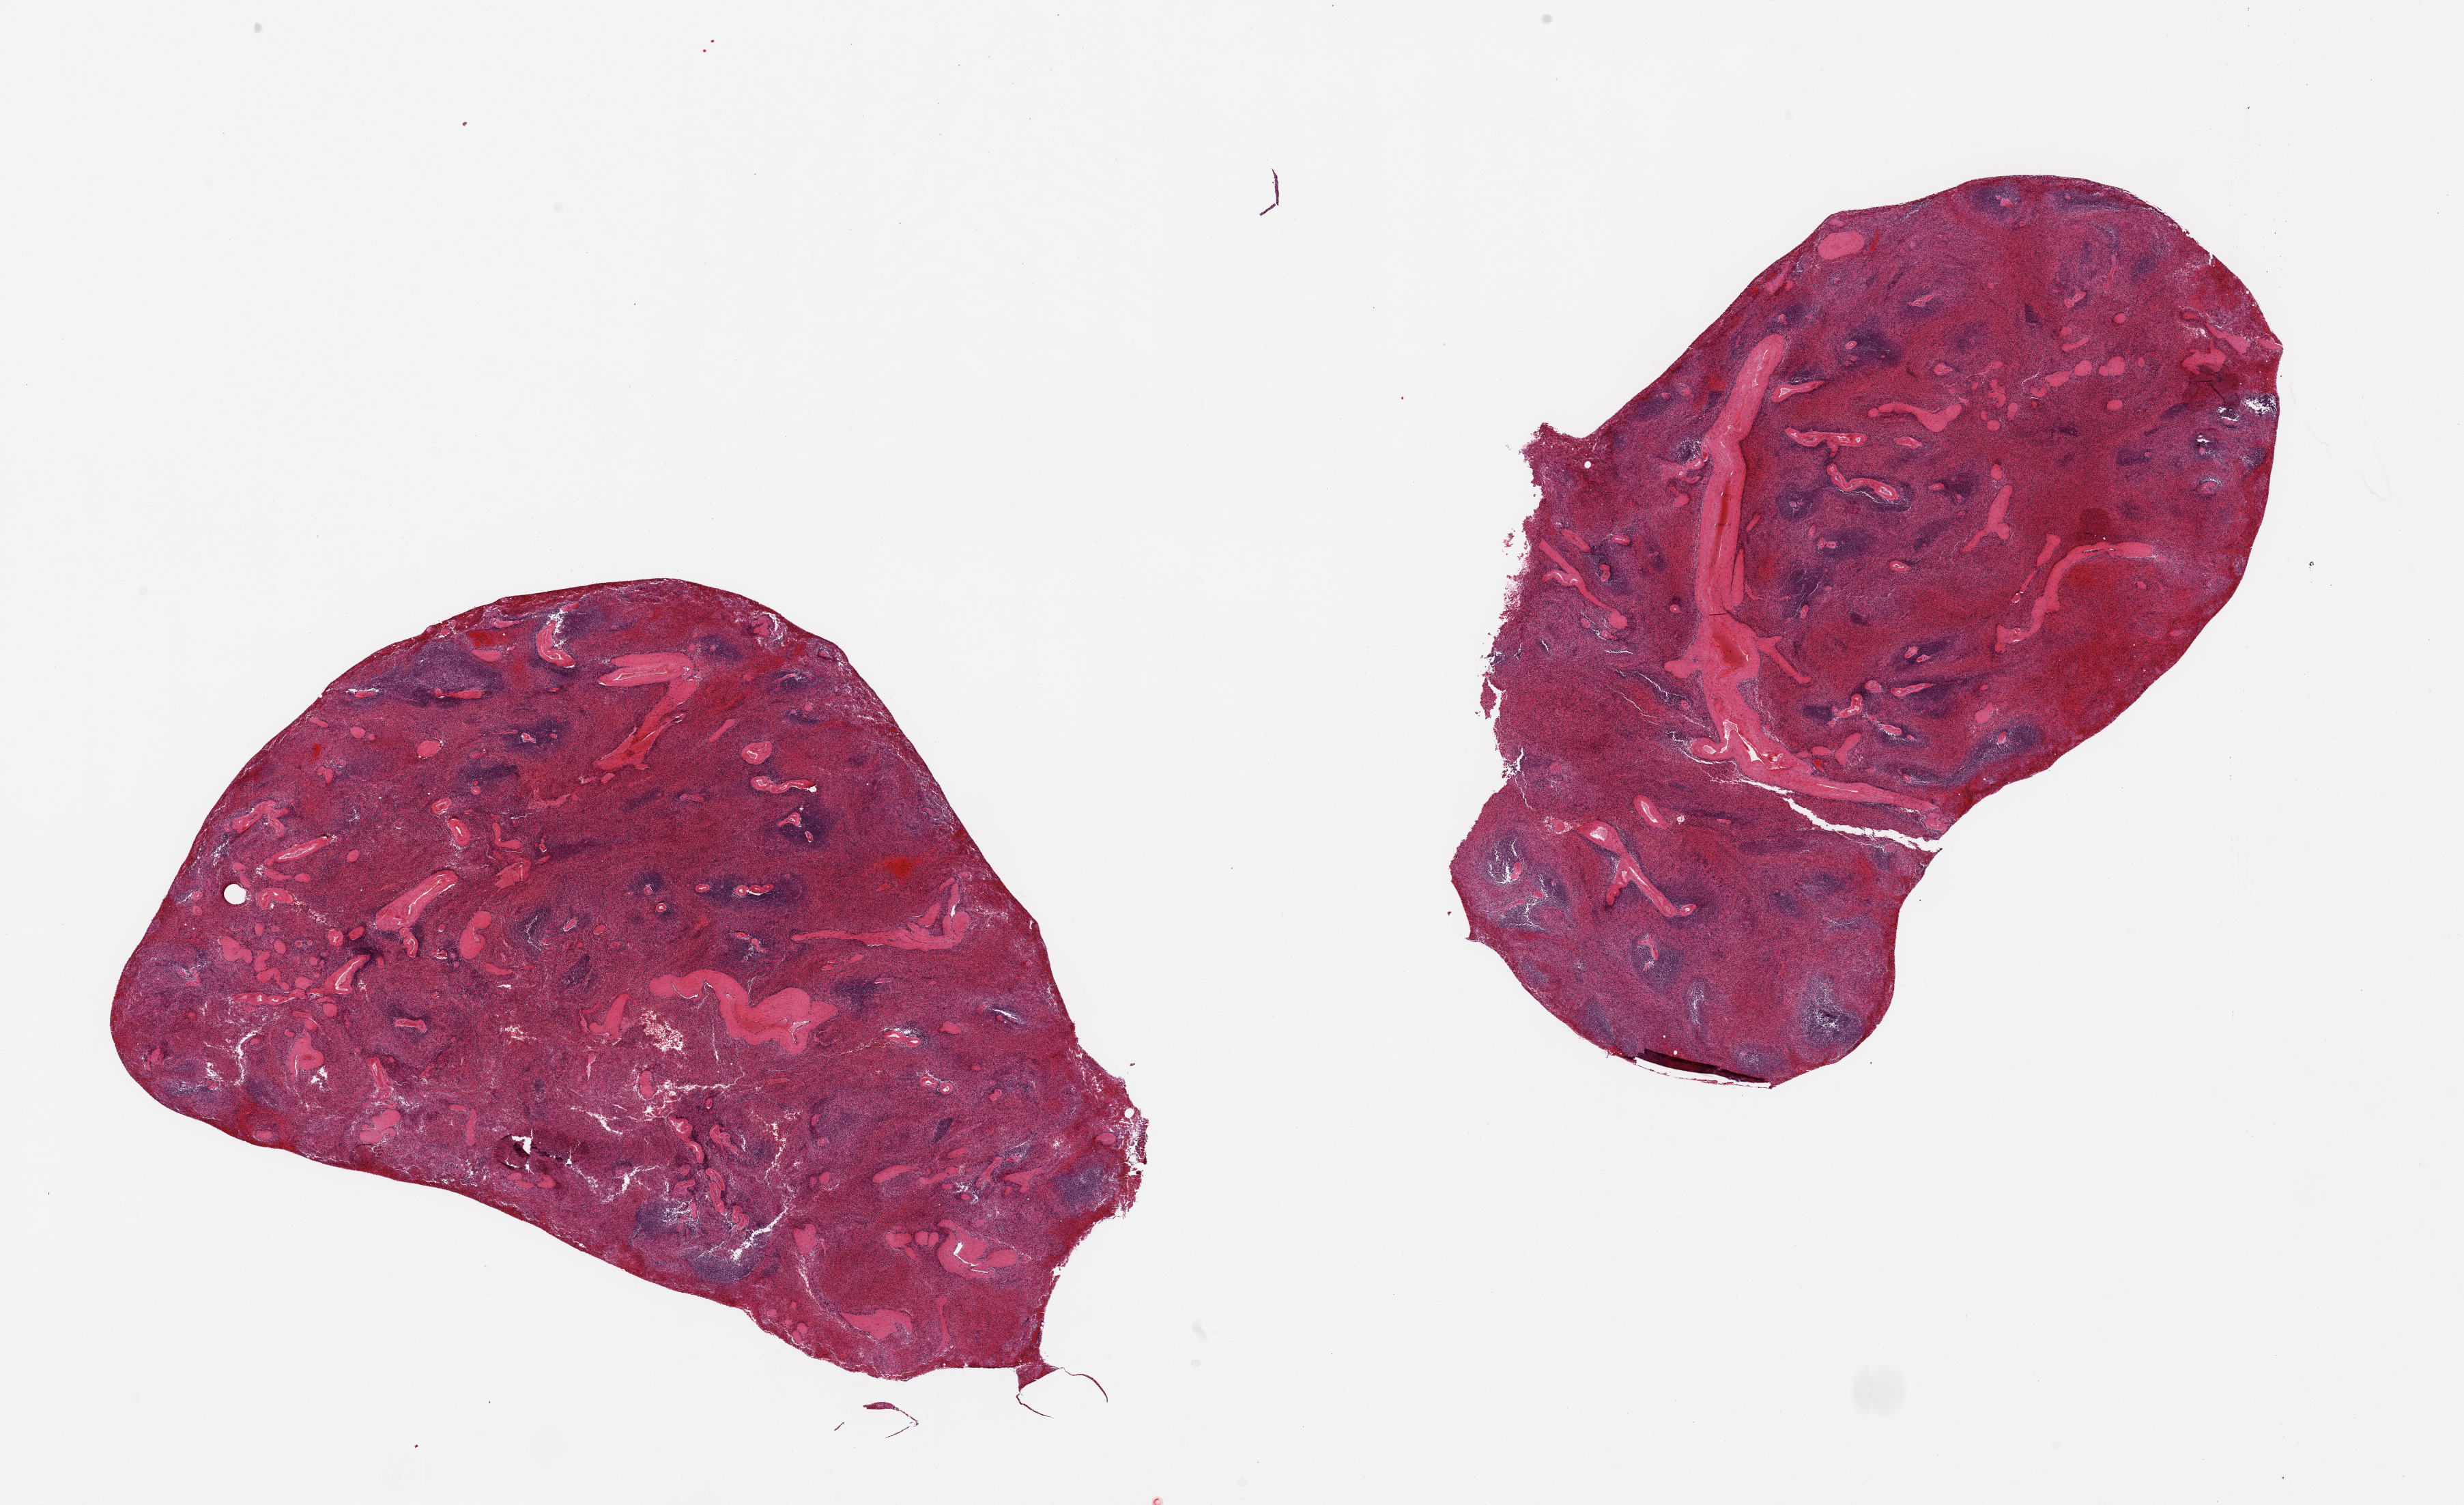
Haematoxylin and eosin whole-slide image — a low-resolution overview of the entire scanned area, about 28.5 x 17.4 mm (from a 20x scan); PAXgene-fixed, paraffin-embedded tissue; target tissue: spleen; donor tissue sample. Male donor.
Reviewer comment on this tissue sample: 2 pieces, congested.